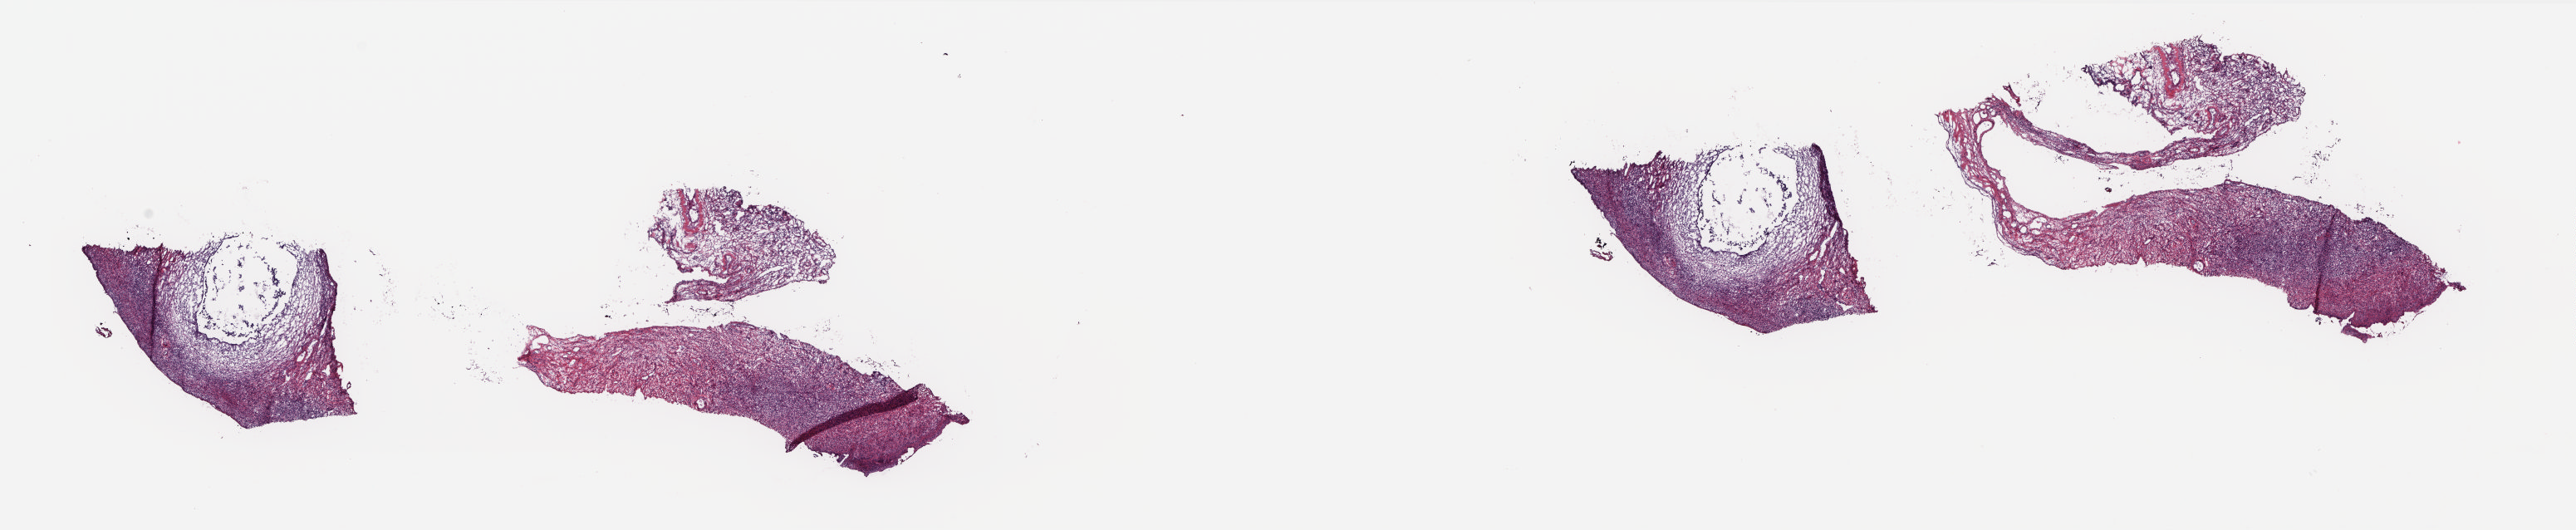
Whole-slide histology image, H&E, whole scanned area (about 25.0 x 5.1 mm) shown as a low-resolution overview, frozen section from the top of the tissue portion, solid tissue normal (non-tumour tissue) sample from the uterus. Patient: female, age at initial diagnosis 41 years. Pathologist review of this section (percent, as recorded): tumour cells 0%, tumour nuclei 0%, normal cells 100%, stromal cells 0%, necrosis 0%. Inflammatory infiltration, as recorded: lymphocyte infiltration 0%, monocyte infiltration 0%, neutrophil infiltration 0%.
This section: solid tissue normal (non-tumour) sample from the same patient. Patient diagnosis: Leiomyosarcoma, NOS.